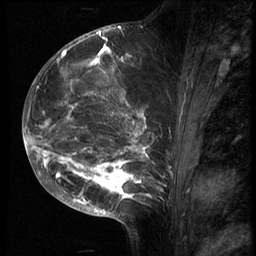
Breast MRI (dynamic contrast-enhanced), one sagittal slice; slice 30 of 70 in the series (ordered by position); 3 images stored at this slice position (order not interpretable as contrast timing); 1.5 T; TE 4.2 ms, TR 9 ms; 2.5 mm slice thickness; 256 × 256 image matrix, field of view 180 × 180 mm. Female patient, age 28 years. Case-level facts recorded for this patient, not image findings: setting: breast cancer imaged before/during neoadjuvant chemotherapy.
Structures marked on this image (semi-automatically segmented with operator editing):
- analysis volume of interest (the breast-tissue region the enhancement analysis was run in; not a lesion): bounding box <43,42,175,215> (left, top, right, bottom; pixels)
- tumour enhancement mask (voxels above the 140 % enhancement threshold inside the analysis volume of interest): <43,48,167,204>